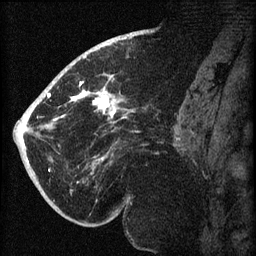
Breast MRI (dynamic contrast-enhanced), one sagittal slice; slice 37 of 60 in the series (ordered by position); dynamic contrast-enhanced series, image 2 of 3 at this slice position (ordered by acquisition); 1.5 T; TE 4.2 ms, TR 8.2 ms; 2 mm slice thickness; 256 × 256 image matrix, field of view 180 × 180 mm. Patient: female, 71 years.
Annotated regions visible in this slice (semi-automatic segmentation, software-assisted and operator-edited):
- analysis volume of interest (the breast-tissue region the enhancement analysis was run in; not a lesion): box from (x=40, y=72) to (x=147, y=196) px
- tumour enhancement mask (voxels above the 70 % enhancement threshold inside the analysis volume of interest): (x=44, y=82)–(x=126, y=165)